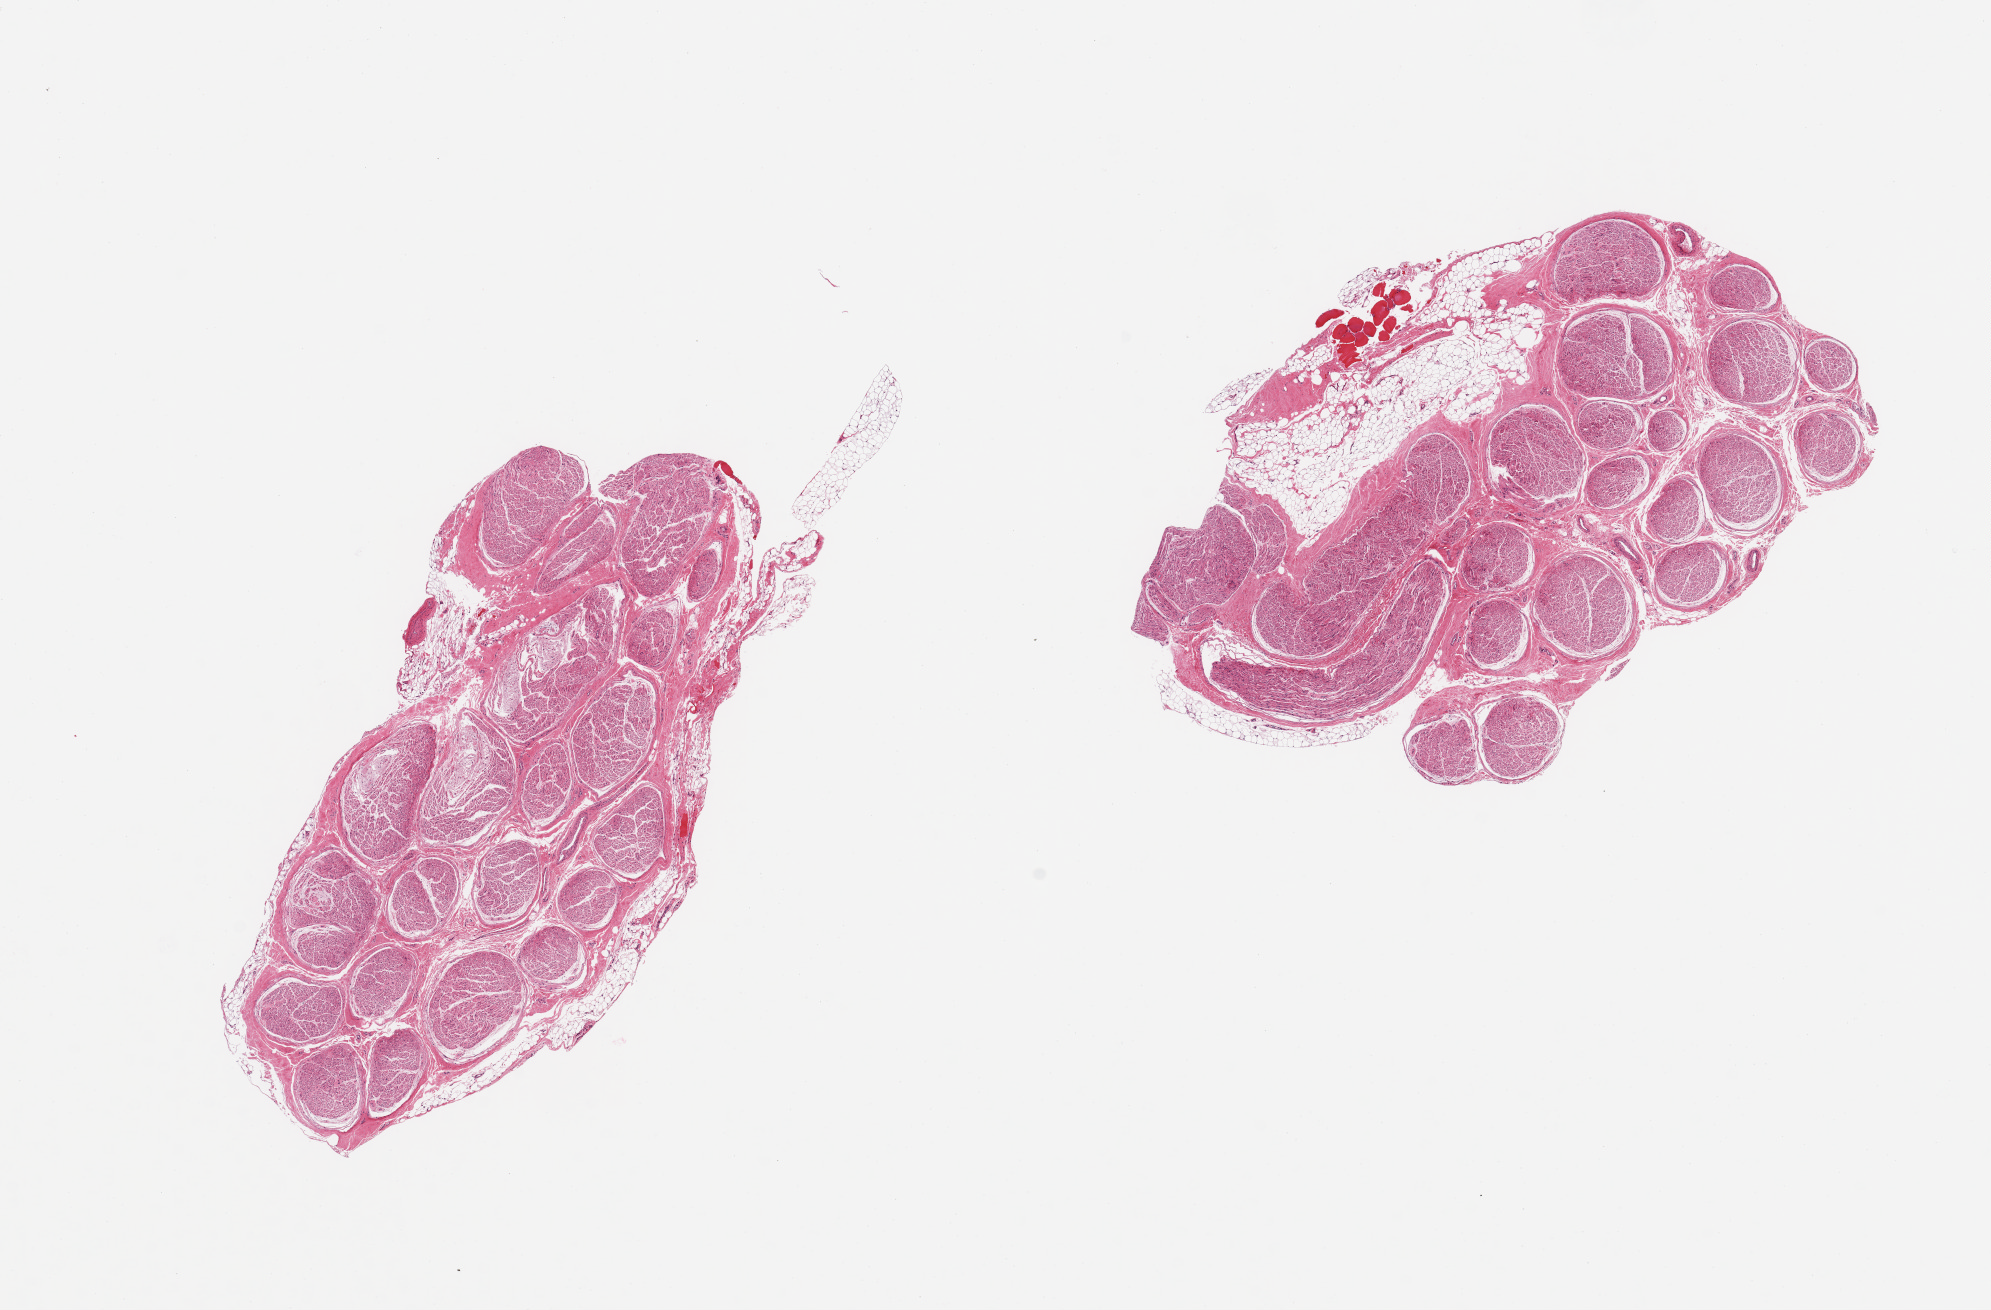
H&E whole-slide image, brightfield — low-resolution overview of the scanned area, about 15.8 x 10.4 mm (from a 20x scan), PAXgene-fixed paraffin-embedded (PFPE) section, target tissue: tibial nerve, tissue donor sample. Donor sex: female.
Review note (as recorded): 2 pieces; 25% external fat & carried-over skeletal muscle in 1.